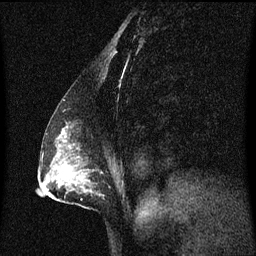
Breast MRI (dynamic contrast-enhanced), one sagittal slice; position 38 of 60 along the scan axis; dynamic contrast-enhanced series, image 2 of 3 at this slice position (ordered by acquisition); 1.5 T; TE 4.2 ms, TR 8.4 ms; 2 mm slice thickness; 256 × 256 image matrix, field of view 200 × 200 mm. Female patient, age 40 years. From the clinical record (not read from this slice): setting: breast cancer imaged before/during neoadjuvant chemotherapy; receptor status: triple-negative.
Outlined on this slice (semi-automatically segmented with operator editing):
- analysis volume of interest (the breast-tissue region the enhancement analysis was run in; not a lesion): bounding box <58,124,117,209> (left, top, right, bottom; pixels)
- tumour enhancement mask (voxels above the 70 % enhancement threshold inside the analysis volume of interest): <64,130,67,139>